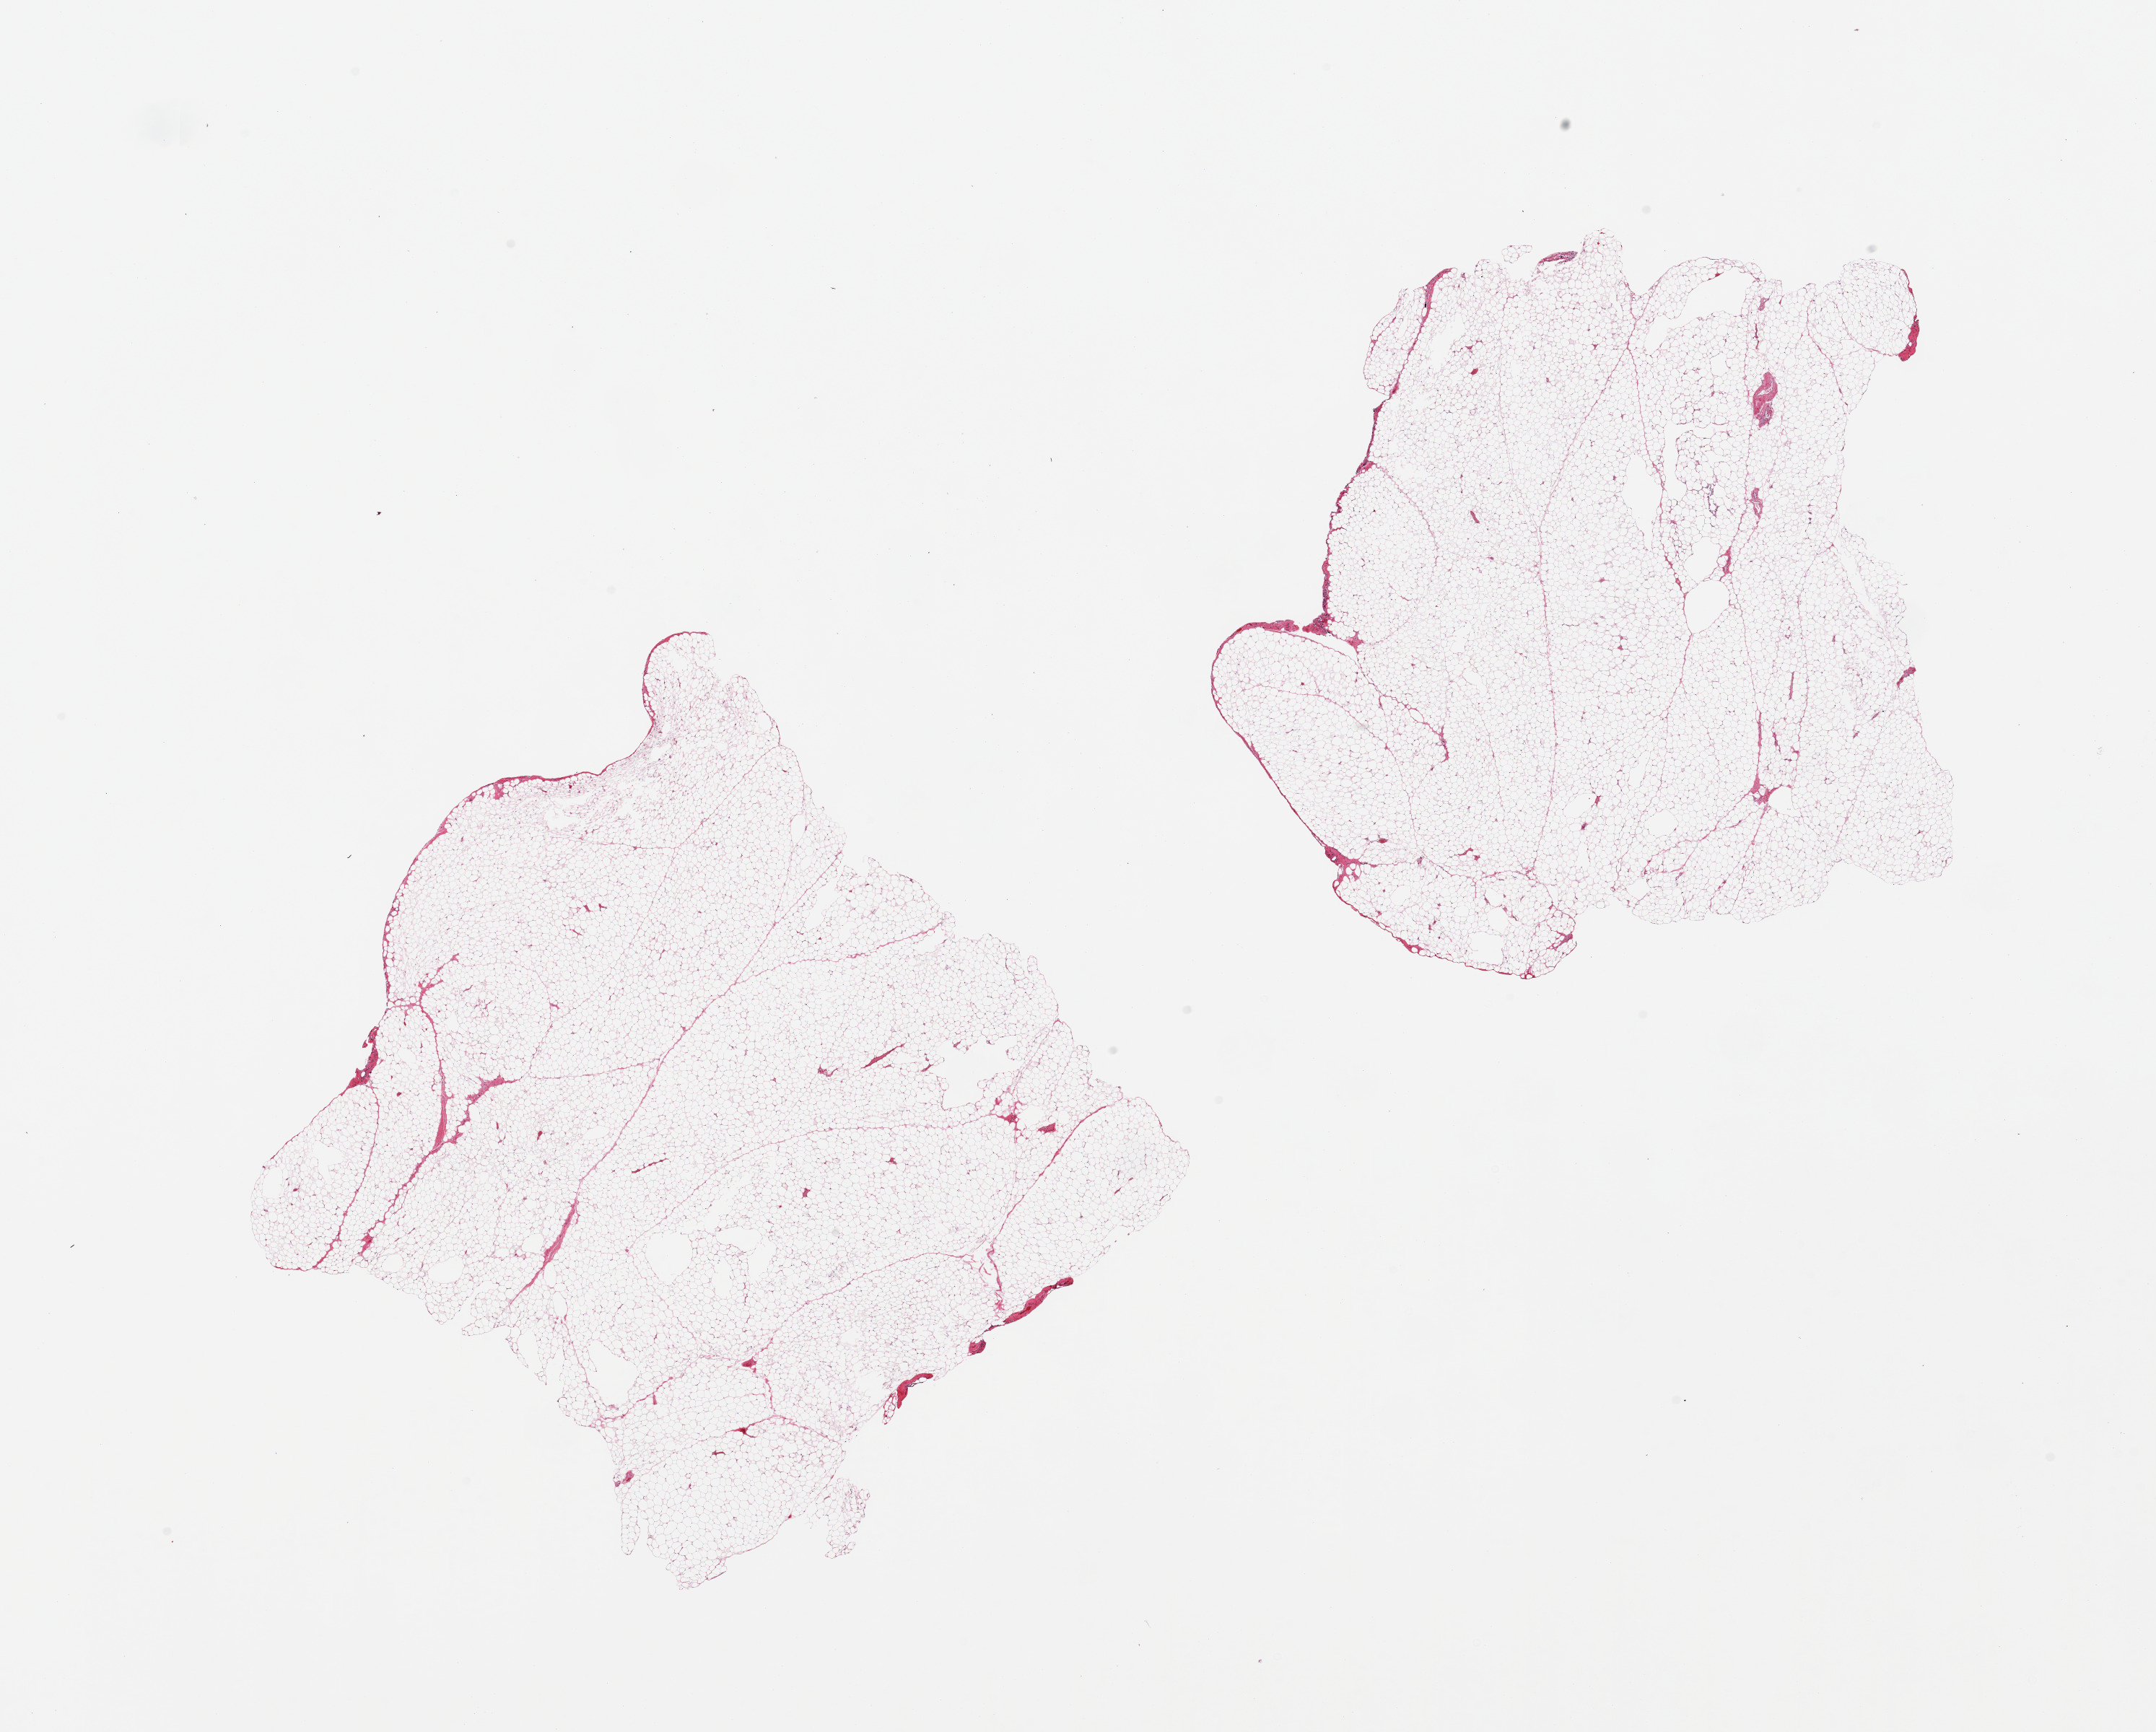
Whole-slide image, H&E stain — shown as a low-resolution overview of the whole scanned area (about 23.6 x 19.0 mm); PAXgene-fixed, paraffin-embedded tissue; section of omentum (target tissue); donor tissue sample. Donor: female.
Review note (as recorded): 2 pieces.